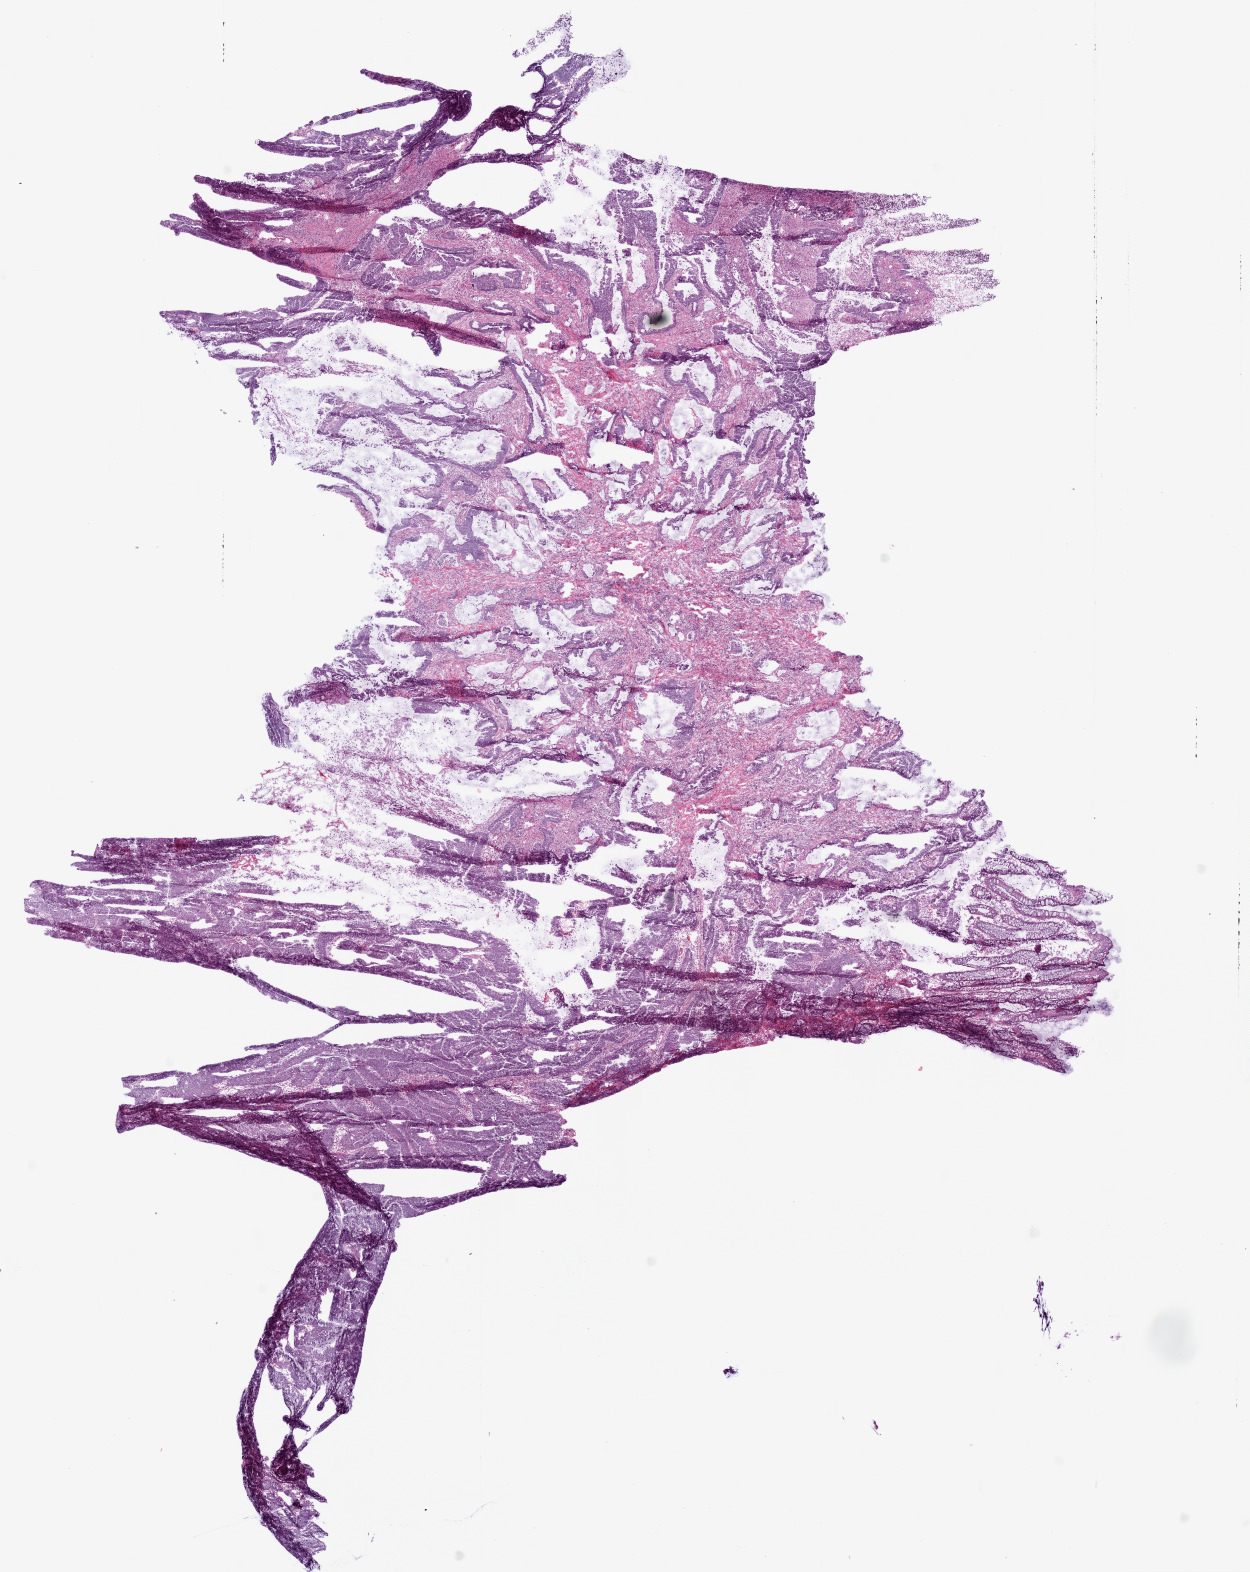
Digitized H&E-stained tissue section (whole slide), whole scanned area (about 10.0 x 12.6 mm, from a 20x scan) shown as a low-resolution overview; frozen section from the bottom of the tissue portion; primary tumour sample from the rectum. Female patient; age at initial diagnosis 76 years. Composition of this section per pathologist review: tumour cells 89%, tumour nuclei 80%.
Diagnosis: Mucinous adenocarcinoma (rectosigmoid junction).